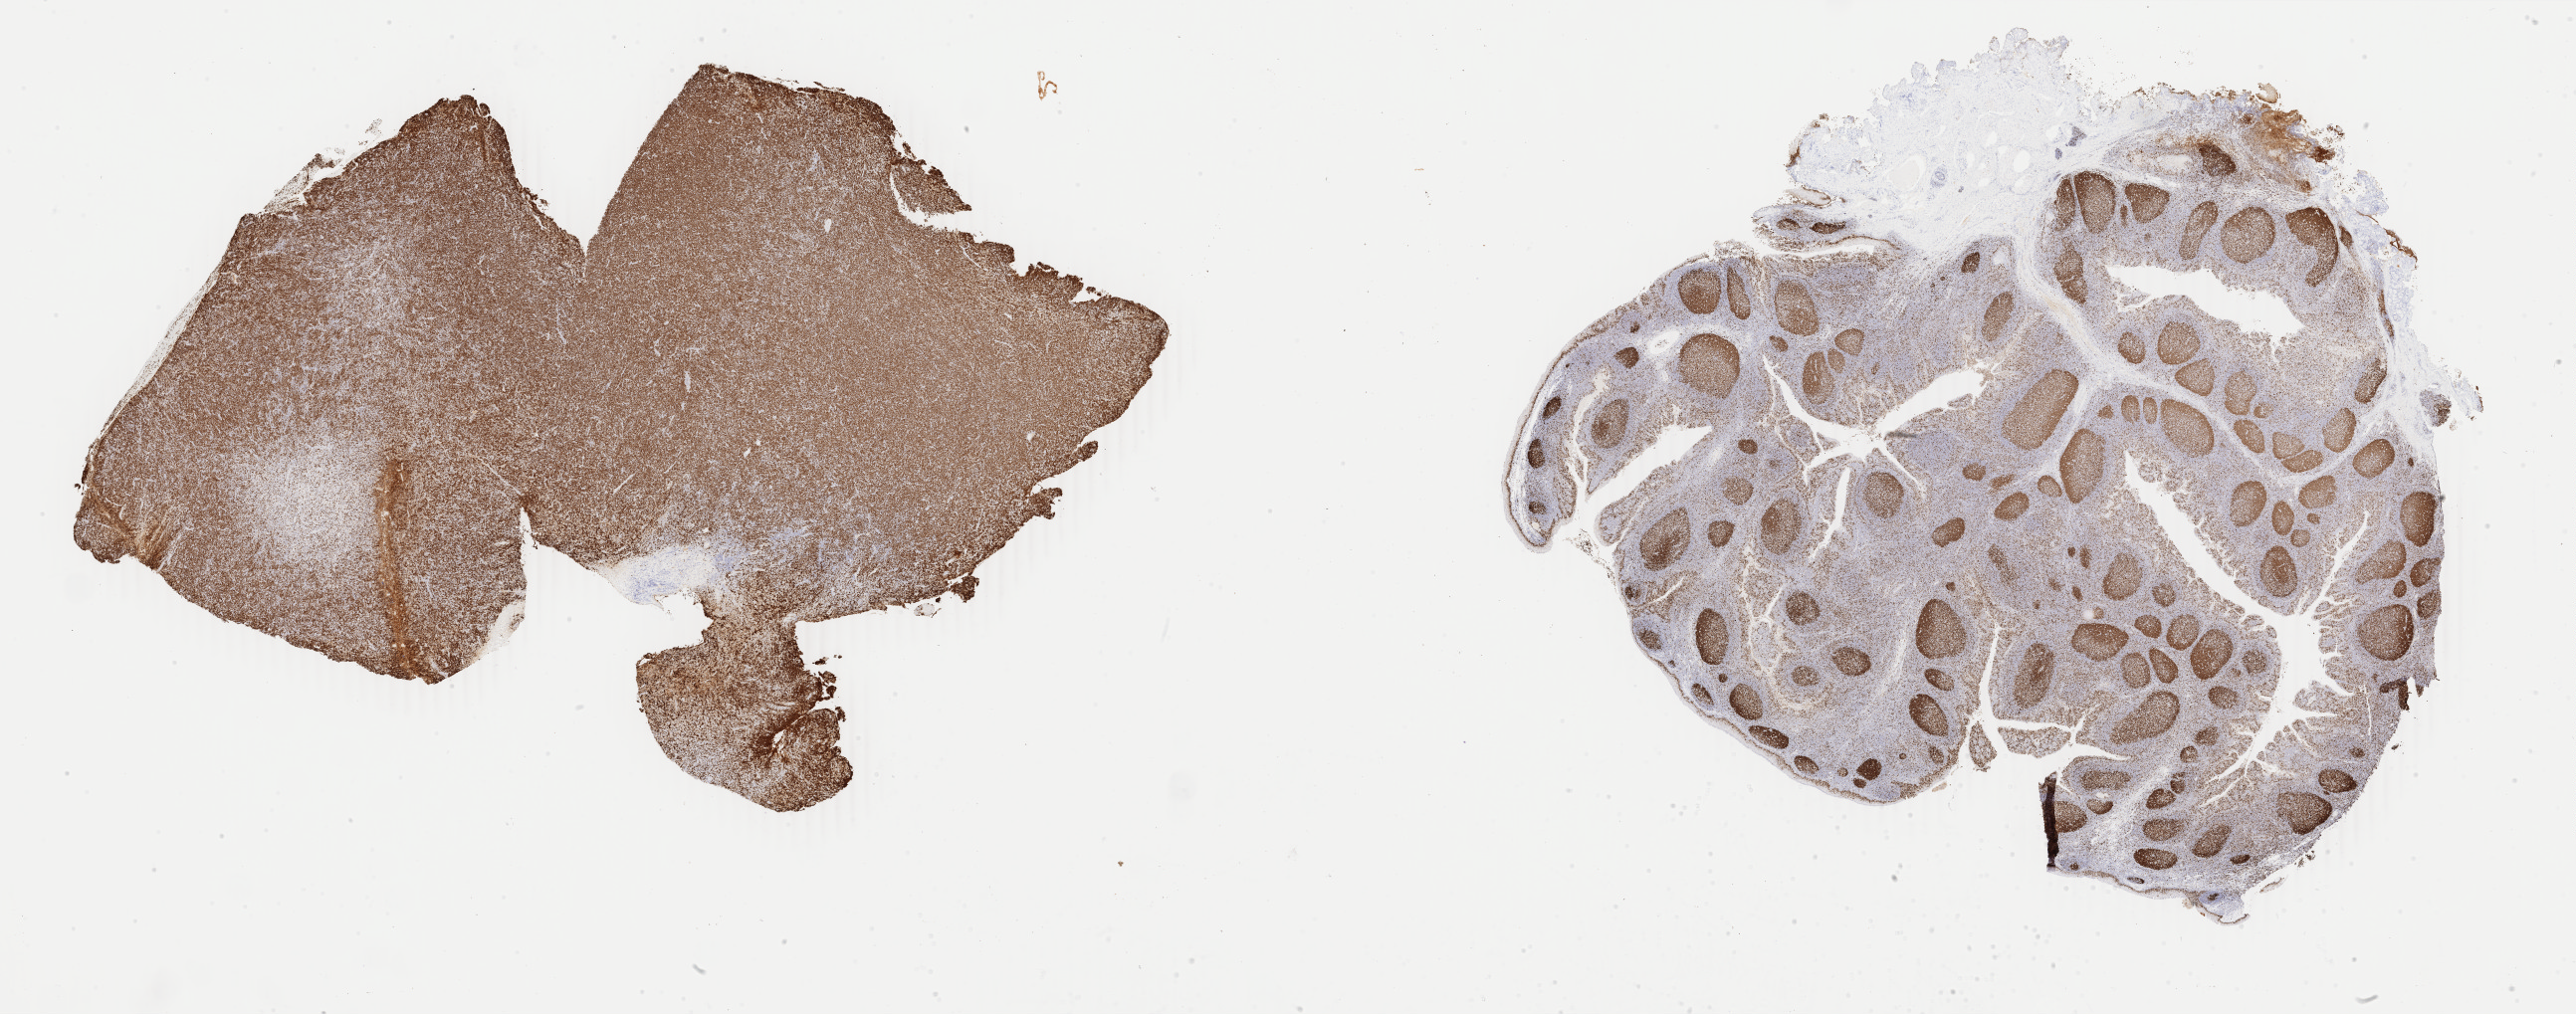
Immunohistochemistry (IHC) whole-slide image stained for Ki-67, low-resolution overview of the scanned area, about 41.2 x 16.2 mm. Specimen: tumor tissue. Patient: male, age at initial diagnosis 7 years.
Diagnosis: Diffuse large B-cell lymphoma, NOS.